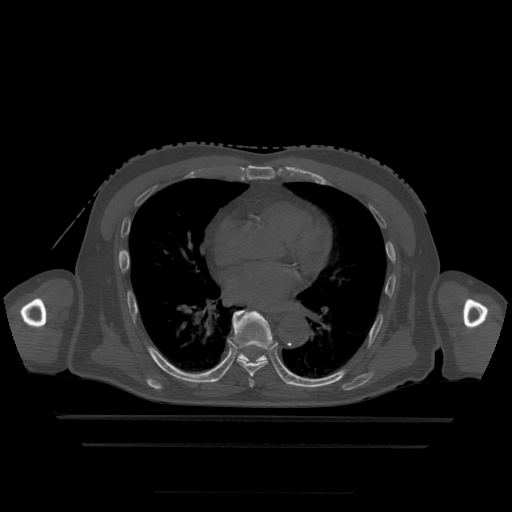
CT including the spine, one axial slice. Position 293 of 522 along the scan axis. Bone window (W 1800 / L 400 HU). 512 × 512 image matrix, field of view 436 × 436 mm. Patient age 68 years. Case-level facts recorded for this patient, not image findings: primary cancer: urothelial.
Annotated regions visible in this slice (semi-automatic segmentation, software-assisted and operator-edited):
- T6 vertebra: bounding box <249,379,255,388> (left, top, right, bottom; pixels)
- T7 vertebra: <233,311,272,378>
- T8 vertebra: <233,316,268,363>